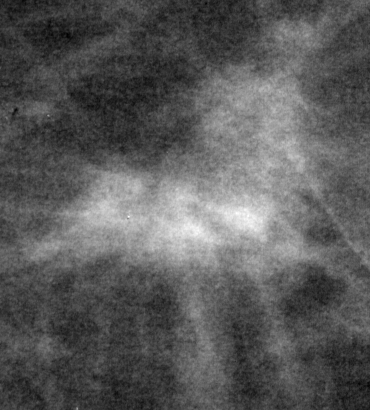
Crop from a digitized film mammogram around one marked abnormality; right breast; CC view.
Marked abnormality: mass, shape irregular, margins spiculated; BI-RADS assessment category 5; subtlety rating 2 on a 1 (subtle) to 5 (obvious) scale; pathology (as recorded): malignant.